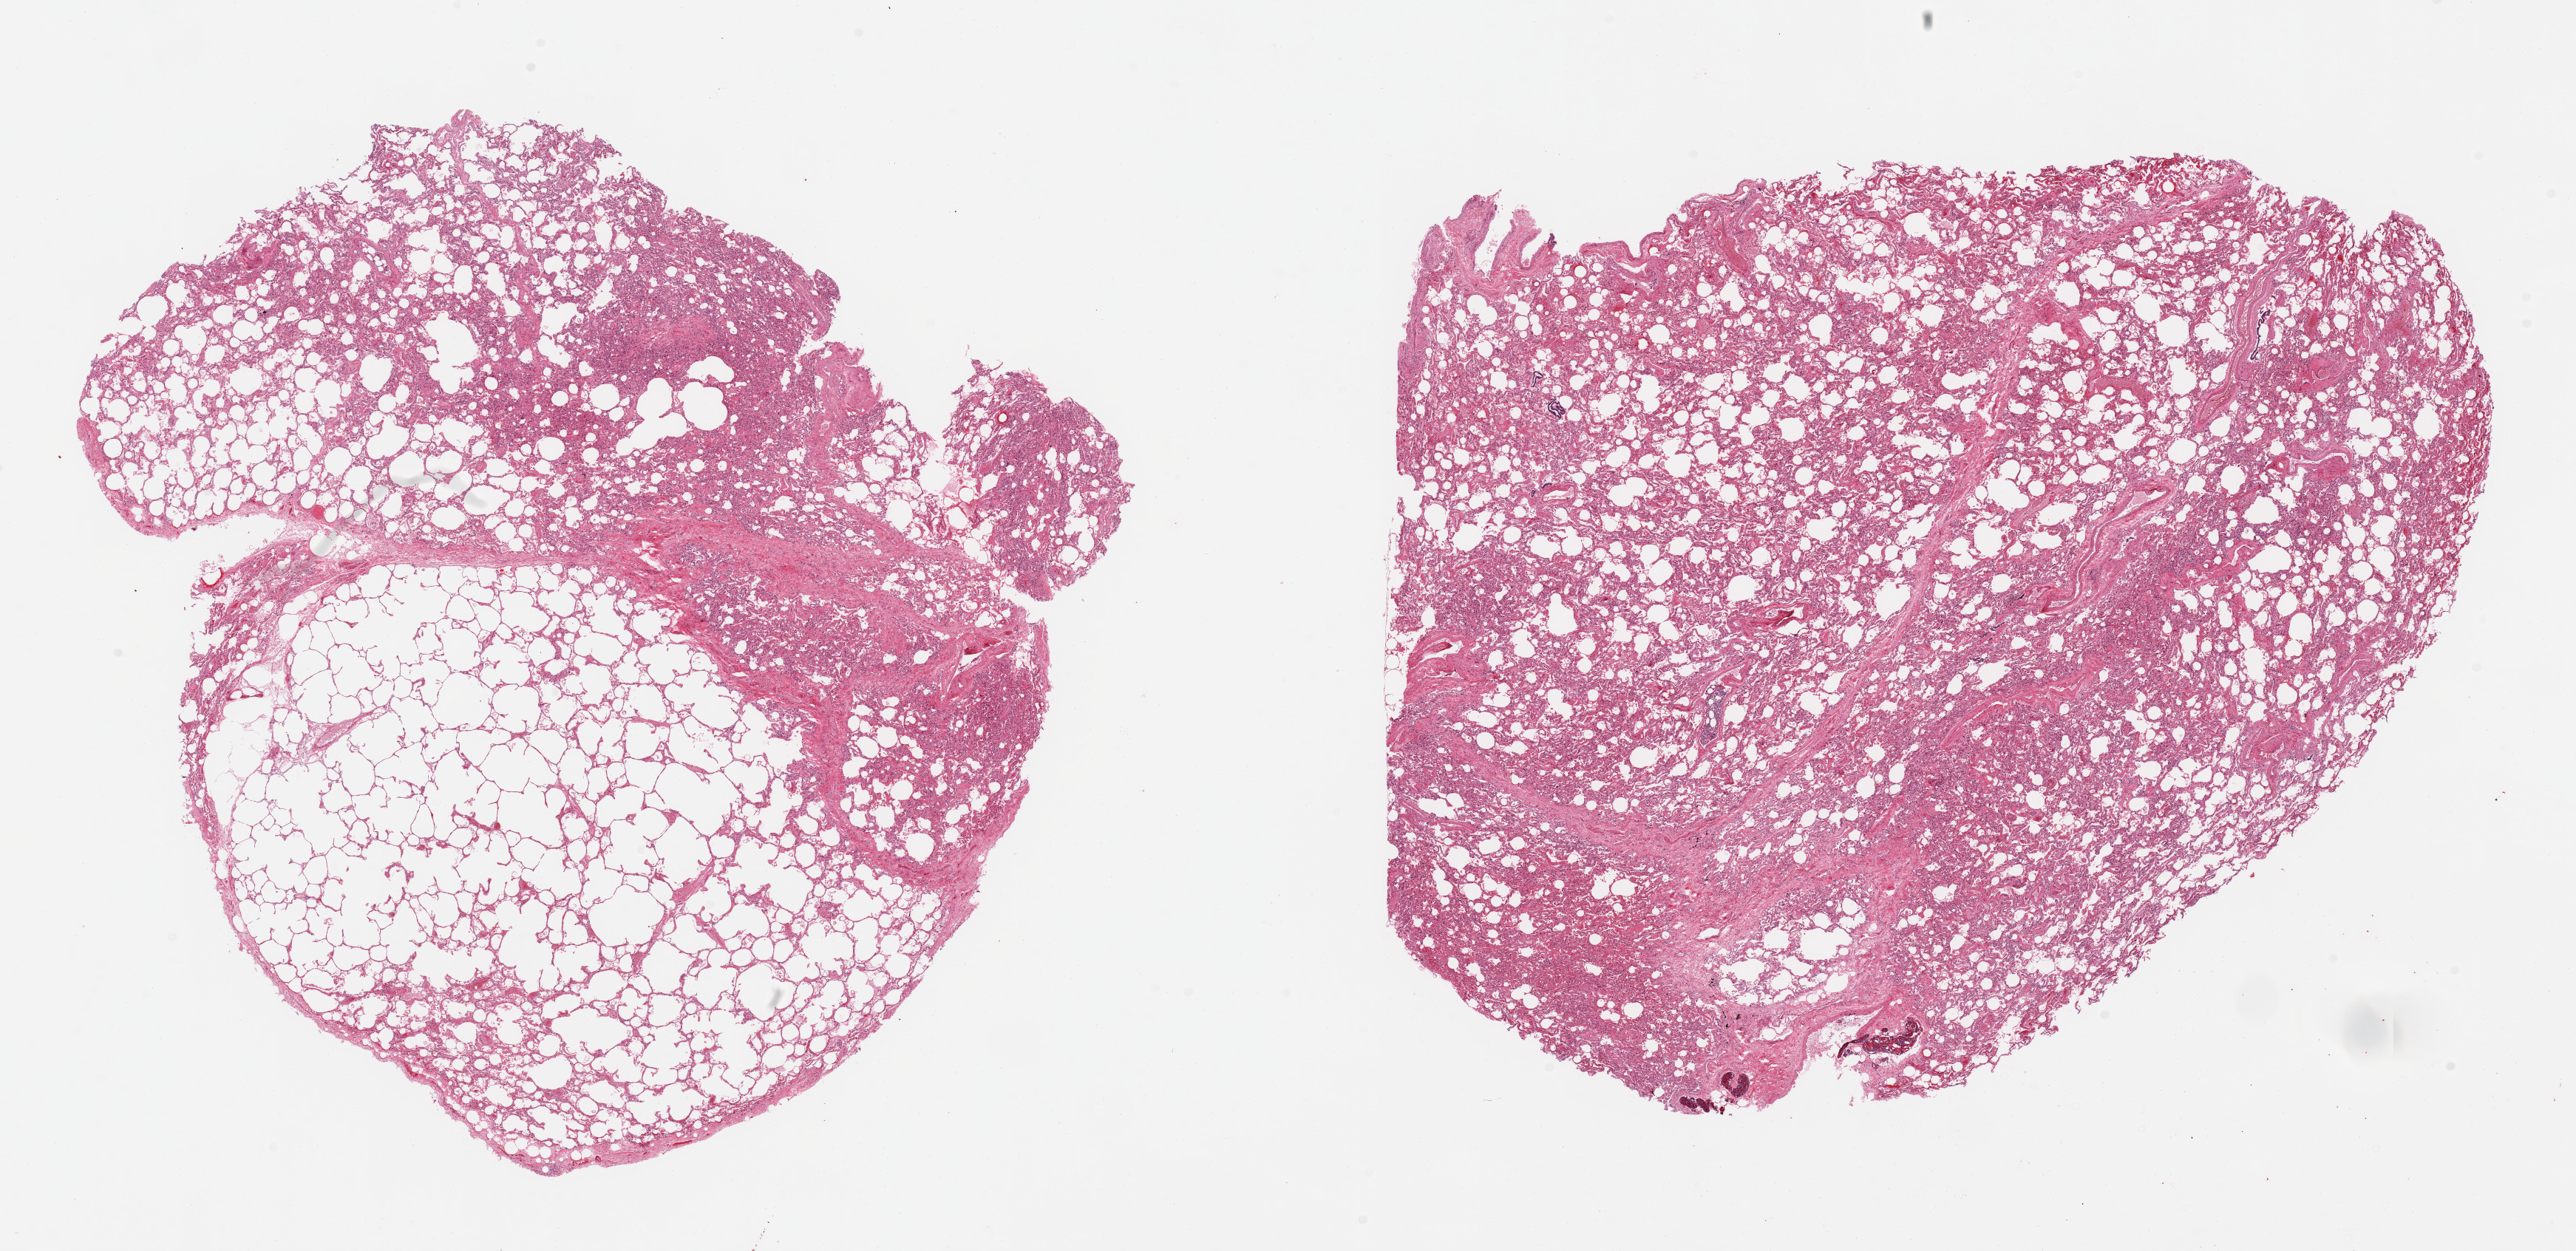
Hematoxylin and eosin (H&E) whole-slide image, brightfield — whole scanned area (about 27.6 x 13.4 mm) shown as a low-resolution overview, PAXgene-fixed, paraffin-embedded tissue, section of lung (target tissue), tissue donor sample. Donor sex: male.
Reviewer comment on this tissue sample: 2 pieces.